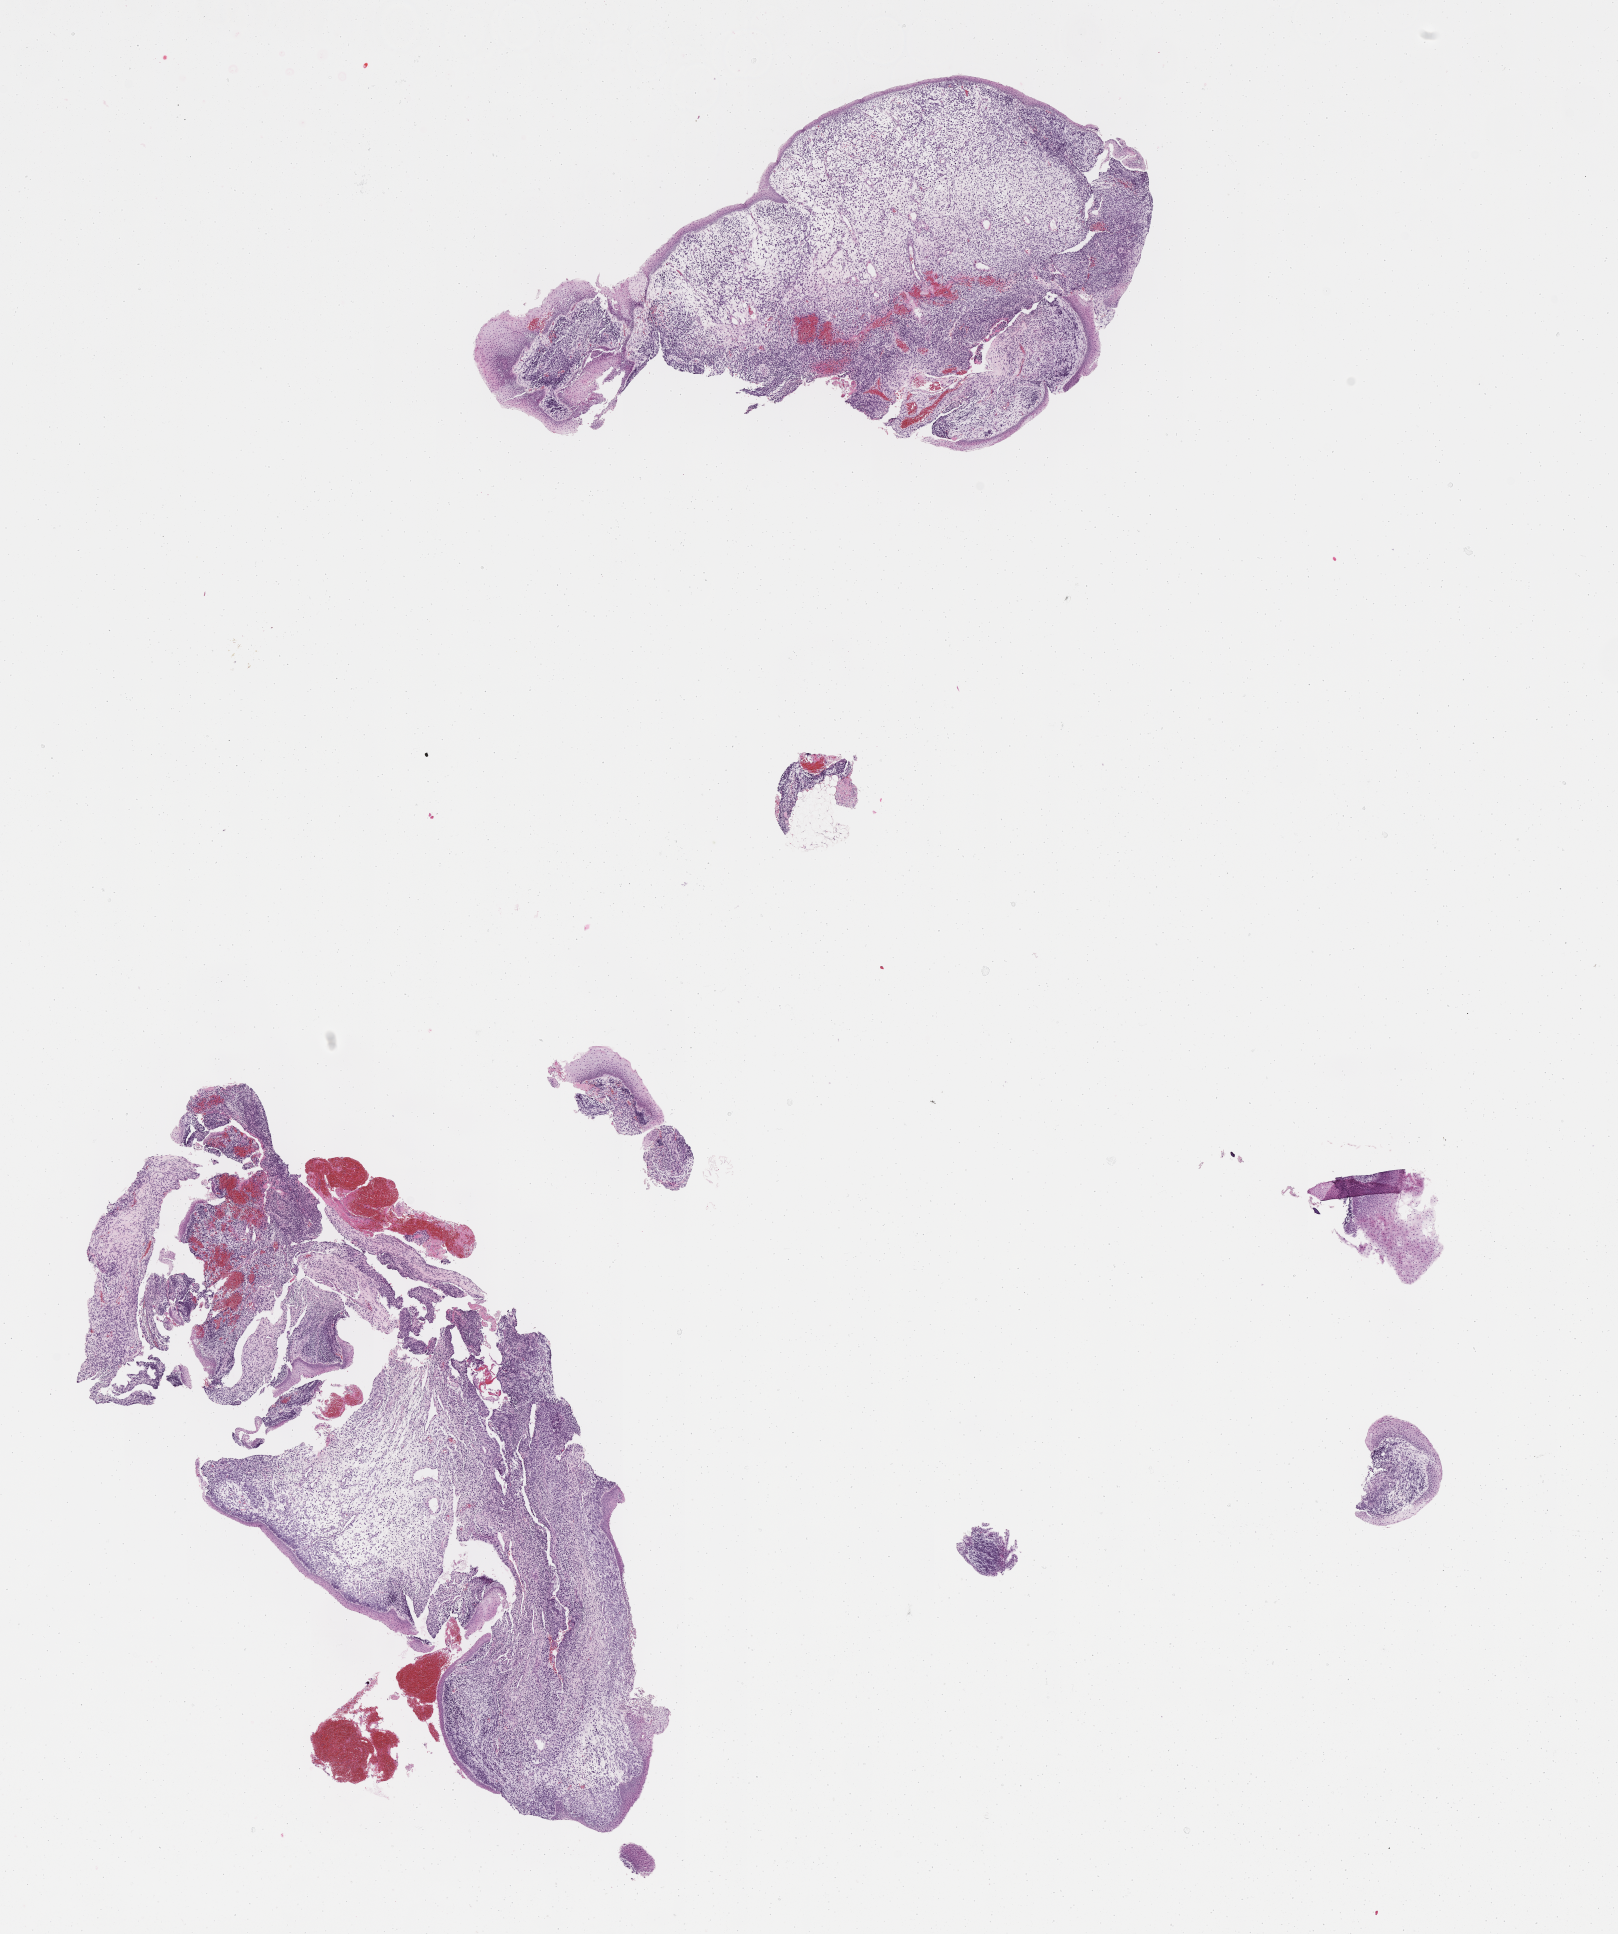
Digitized haematoxylin and eosin-stained section of tumor tissue — low-resolution overview of the scanned area, about 13.1 x 15.6 mm. FFPE section. Female patient, age at diagnosis 1.5 years.
Diagnosis: rhabdomyosarcoma; histological classification: botryoid. Stage (as recorded): 1. Metastatic status at presentation (as recorded): non-metastatic.